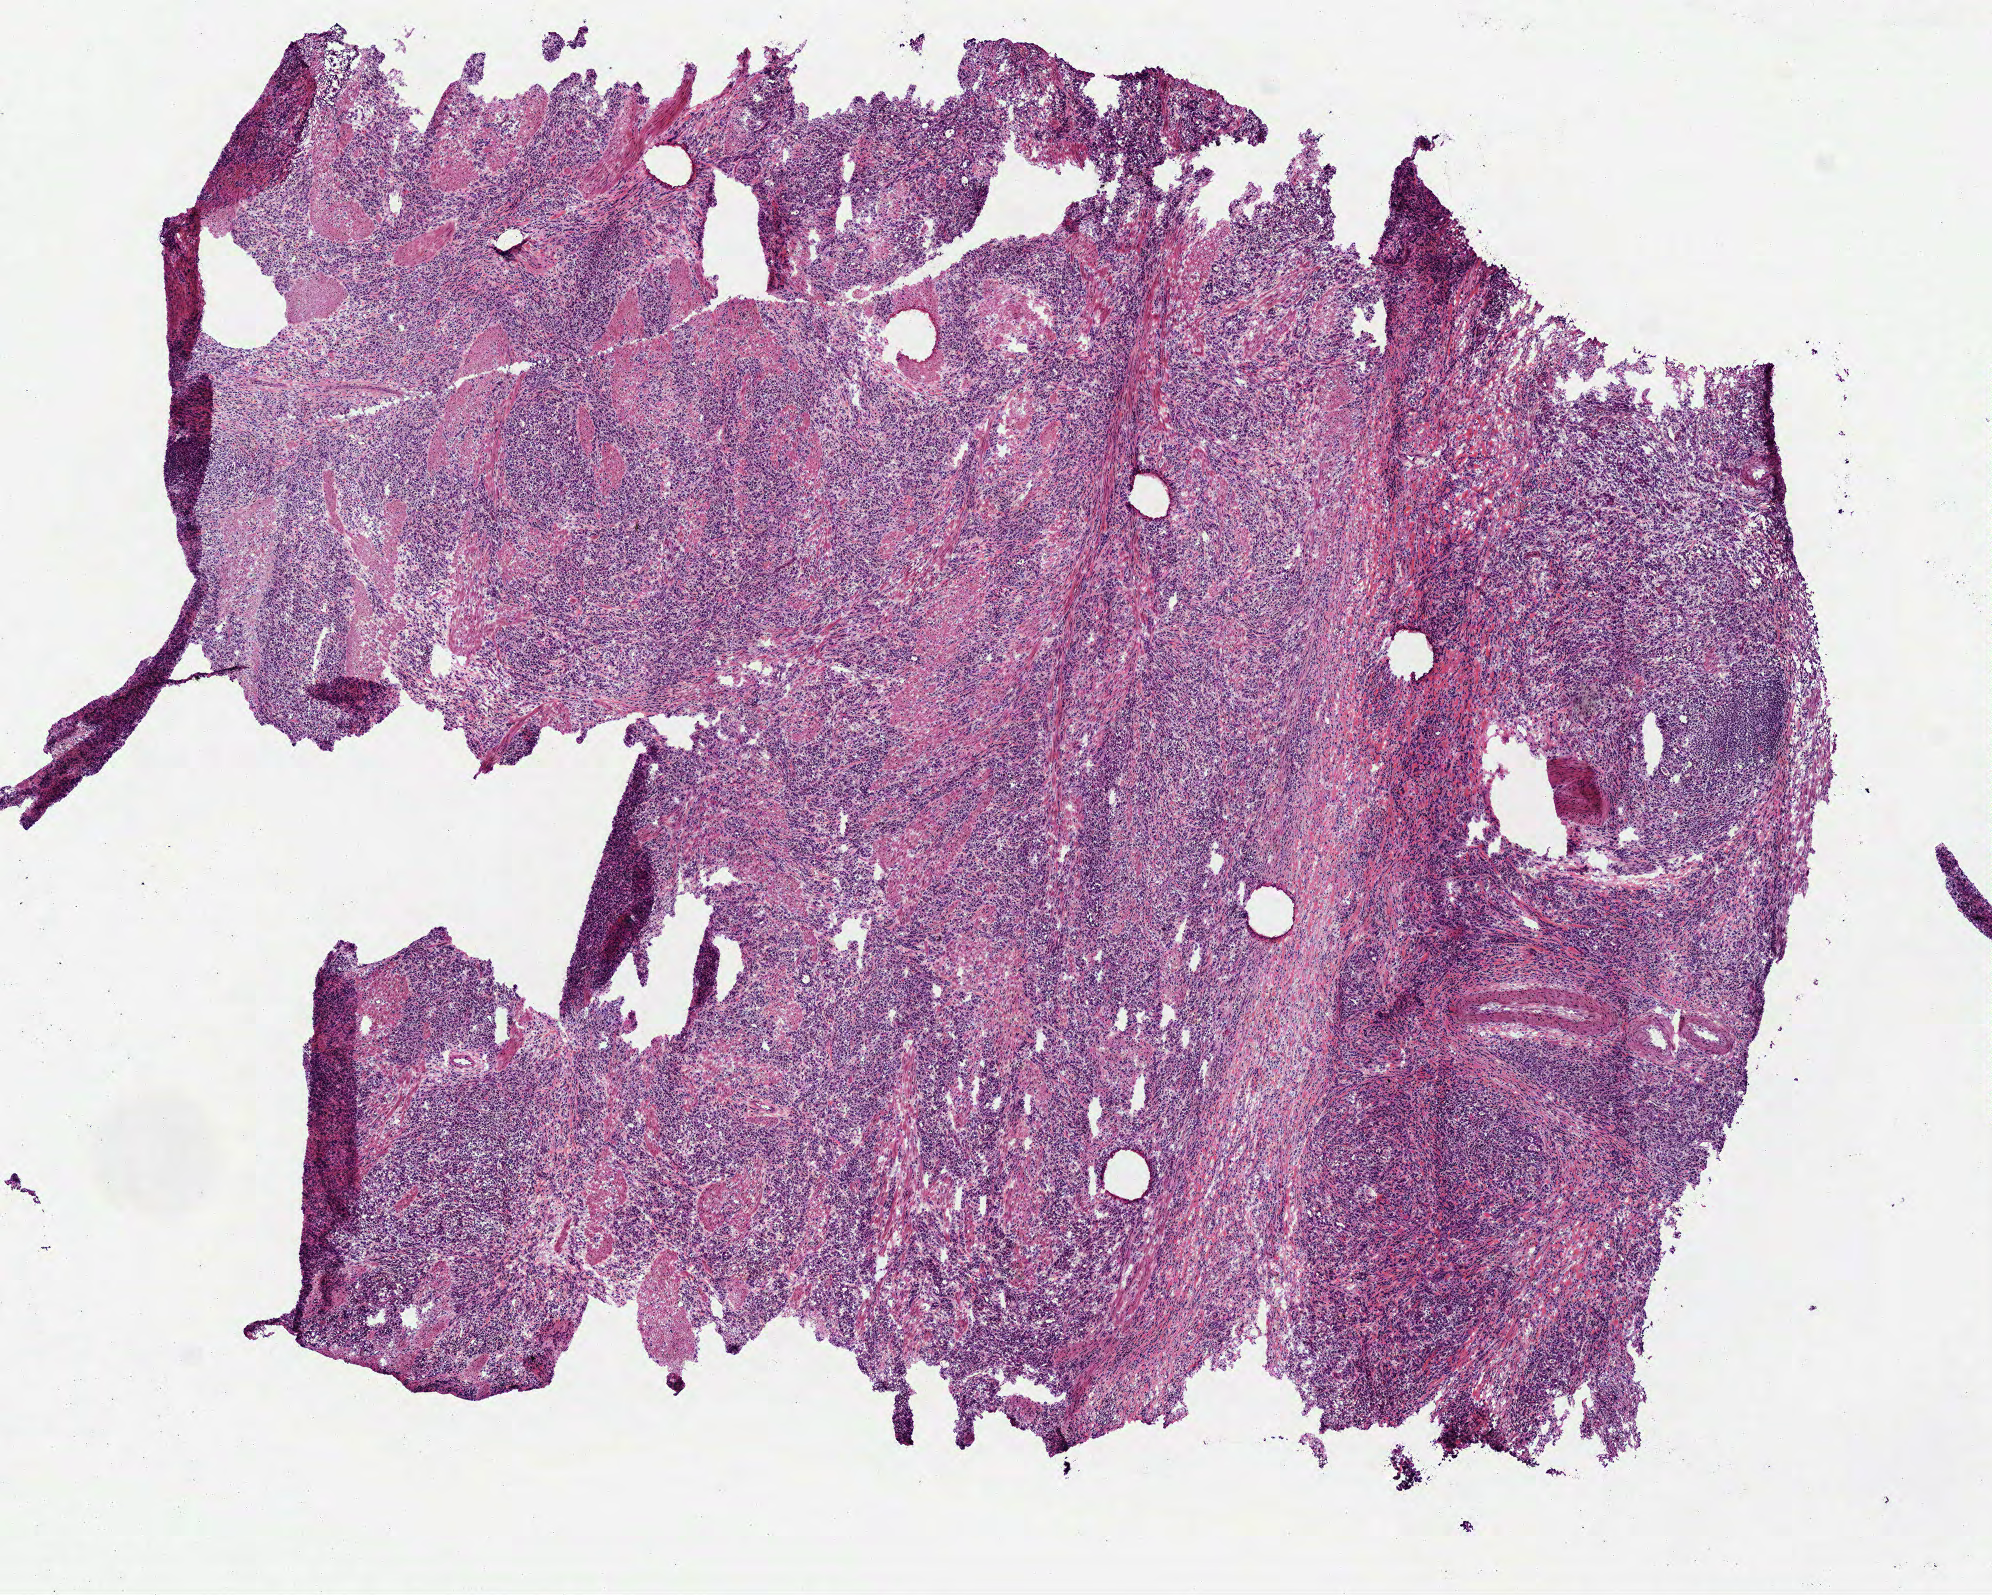
Whole-slide histology image, Hematoxylin and eosin (H&E) stained, low-resolution overview of the scanned area, about 8.0 x 6.4 mm (from a 40x scan), frozen section from the bottom of the tissue portion, stomach, primary tumour sample. Male, age 77 years at initial diagnosis. Histologic grade: G3 (poorly differentiated).
- TNM: T4a N3a MX
- histologic diagnosis: Carcinoma, diffuse type (body of stomach)
- AJCC pathologic stage: IIIC
- lymph nodes positive (case pathology): 14 of 30 examined